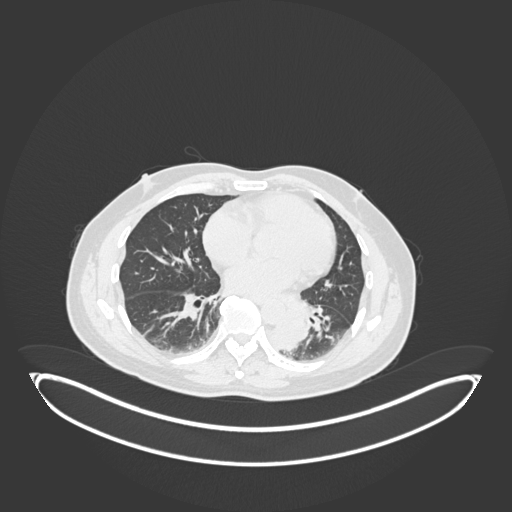
Chest CT, one axial slice. Position 78 of 258 along the scan axis. 120 kVp. Lung window (W 1500 / L -600 HU). 512 × 512 image matrix, field of view 500 × 500 mm. Patient: male, 54 years. Case-level facts recorded for this patient, not image findings: clinical TNM (as recorded): T3 N0 M0.
Annotated regions visible in this slice (rectangle marked by the reading radiologist):
- lung tumour (recorded histology: squamous cell carcinoma): bounding box (x1, y1, x2, y2) in pixels: (265, 305, 310, 352)